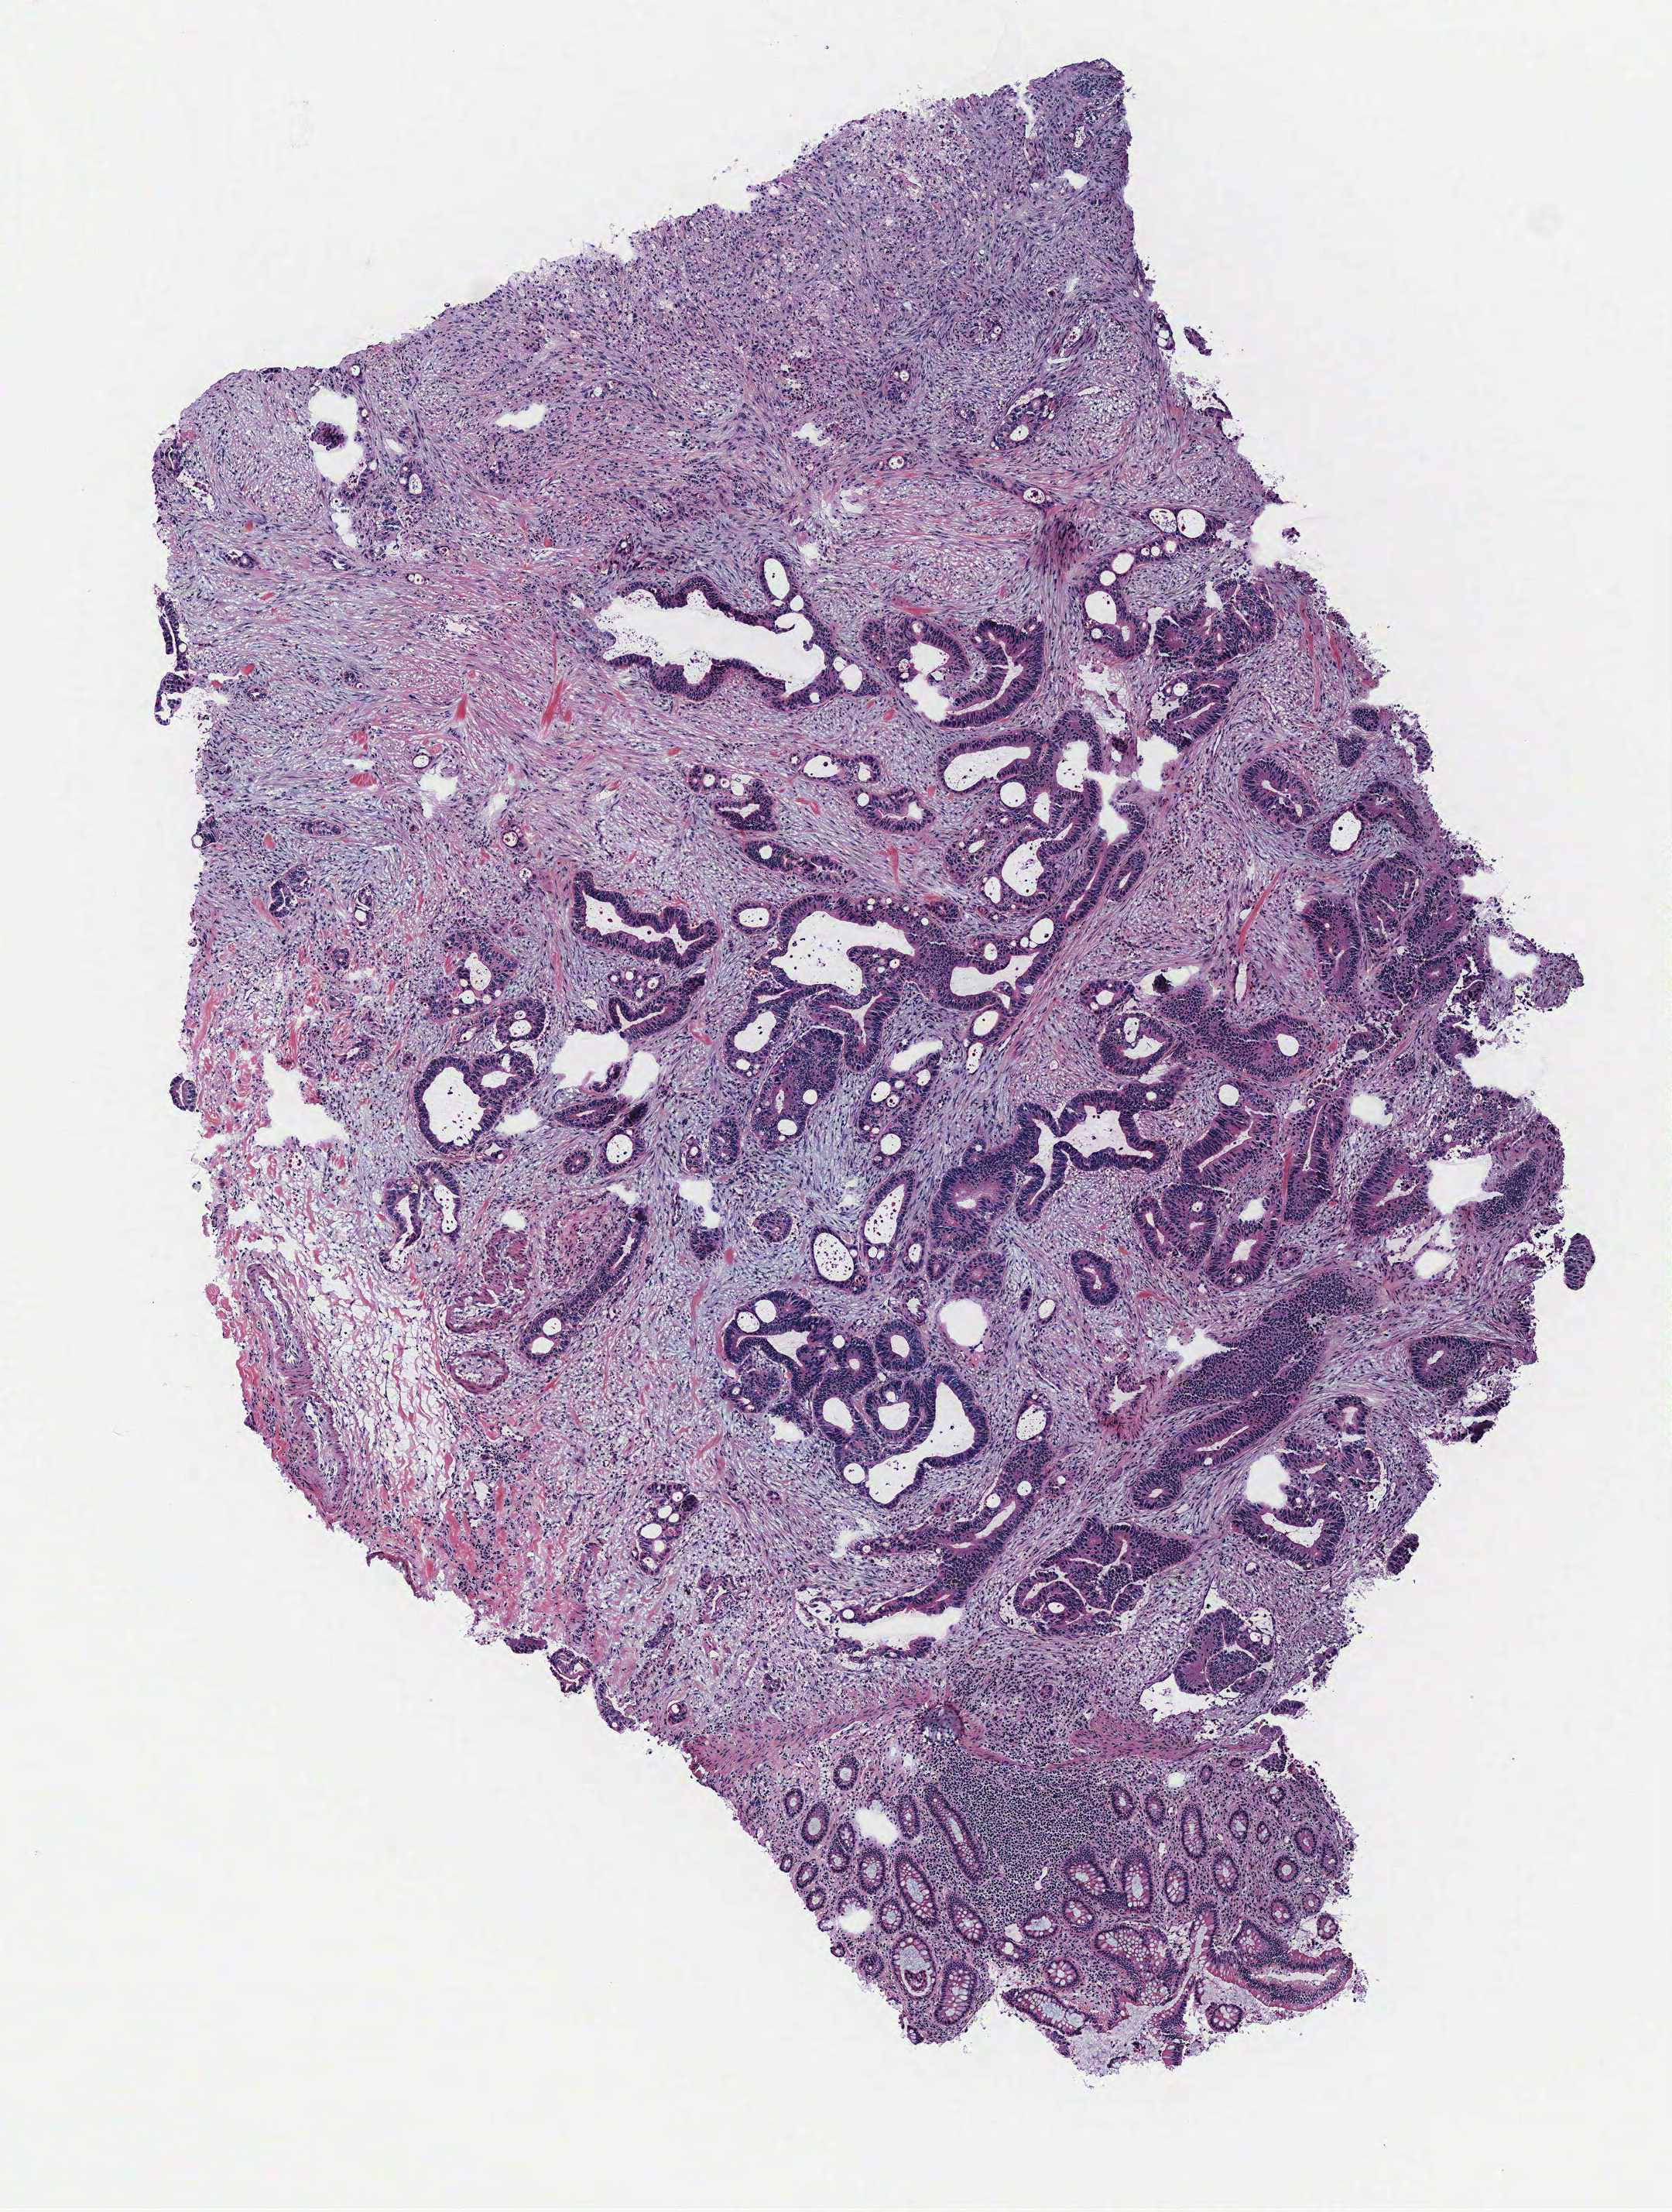
Digitized H&E tissue section (whole slide), whole scanned area (about 4.3 x 5.7 mm, slide scanned at 40x) shown as a low-resolution overview. Colon, tissue type not recorded.
Patient diagnosis (cohort enrolment): colon cancer (colon).